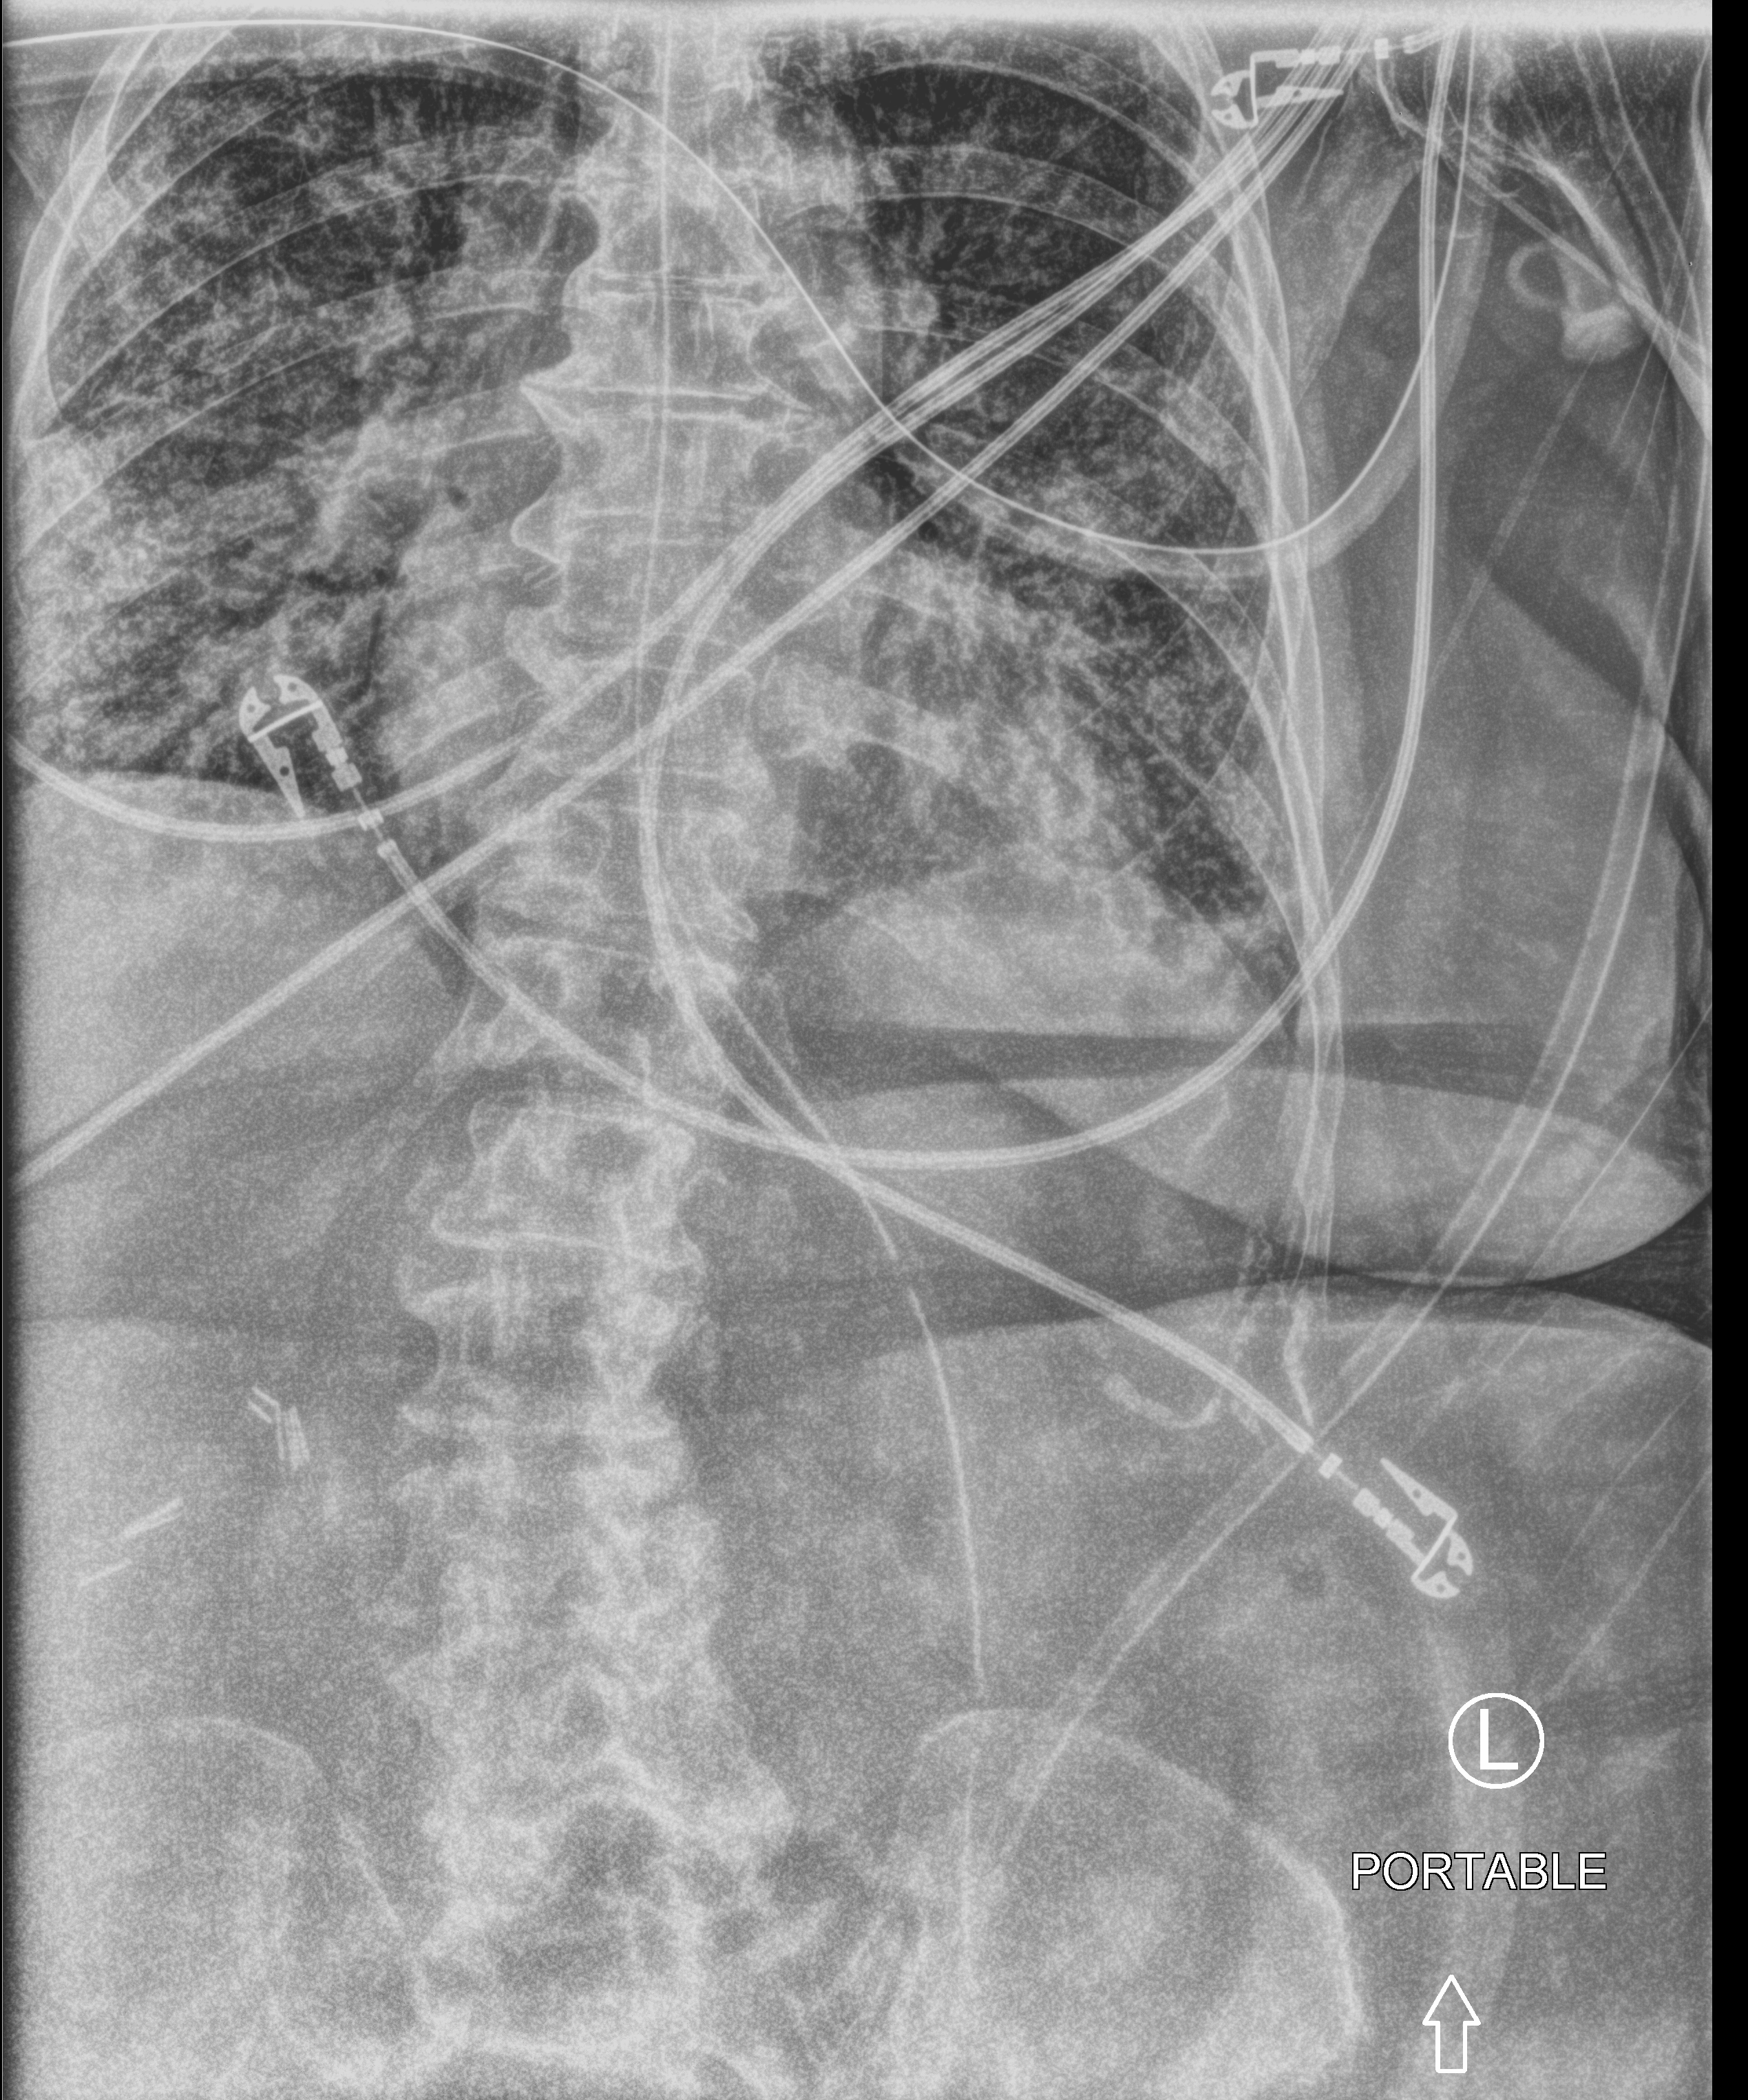
Portable abdomen radiograph, anteroposterior (AP) projection. Patient hospitalised with COVID-19; female, aged 75–90 years.
Admission-level facts for this patient (not findings on this image; timing relative to this image not recorded):
- length of hospital stay: 56 days
- diabetes (admission record): no
- admitted to intensive care during this hospital stay: no